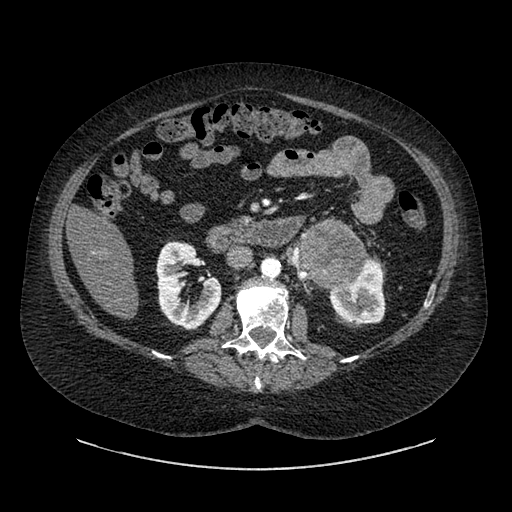
Contrast-enhanced abdominal CT, one axial slice. Position 508 of 769 along the scan axis. Reconstruction kernel SOFT. Intravenous contrast given. Soft-tissue window (W 400 / L 40 HU). 512 × 512 image matrix, field of view 460 × 460 mm. Patient: female, 61 years. Case-level facts recorded for this patient, not image findings: diagnosis: adrenocortical carcinoma; tumour side: left adrenal; tumour size at pathology: 13 cm; Ki-67 index: 79 %; stage (as recorded): 2.
Annotated regions visible in this slice (semi-automatic segmentation, software-assisted and operator-edited):
- mass: bounding box <298,225,363,286> (left, top, right, bottom; pixels)